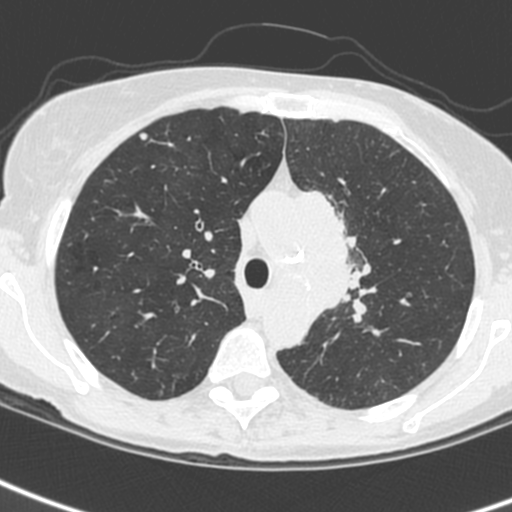
Low-dose screening chest CT, one axial slice. Slice 177 of 242 in the series (ordered by position). Lung window (W 1500 / L -600 HU). 512 × 512 image matrix, field of view 284 × 284 mm.
Structures marked on this image (expert manual segmentation):
- lesion 3 (tumor, upper lobe of left lung): bounding box <301,190,355,312> (left, top, right, bottom; pixels)